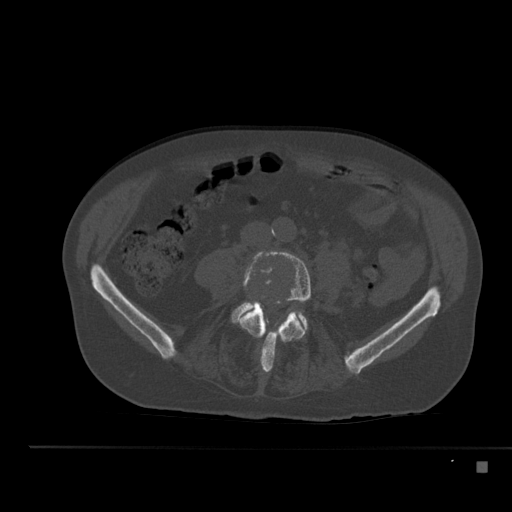
CT including the spine, one axial slice; position 138 of 517 along the scan axis; 120 kVp; bone window (W 1800 / L 400 HU); 1.5 mm slice thickness; 512 × 512 image matrix, field of view 408 × 408 mm. Male patient, age 70 years. Case-level facts recorded for this patient, not image findings: primary cancer: renal; vertebrae with lytic lesions (as recorded): T4, T6, T10, T12, L3, L4, L5.
Structures marked on this image (semi-automatically segmented with operator editing):
- L4 vertebra: bounding box <239,250,311,372> (left, top, right, bottom; pixels)
- L5 vertebra: <232,301,308,326>